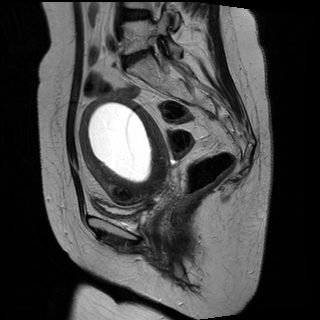
Pelvic MRI for cervical cancer, one sagittal slice; slice 18 of 29 in the series (ordered by position); T2-weighted; 1.5 T; TE 89 ms, TR 2930 ms; 4 mm slice thickness; 320 × 320 image matrix, field of view 260 × 260 mm. Patient: female, 49 years.
Outlined on this slice (outlined manually by an expert reader):
- uterus and cervix: box from (x=78, y=96) to (x=169, y=211) px